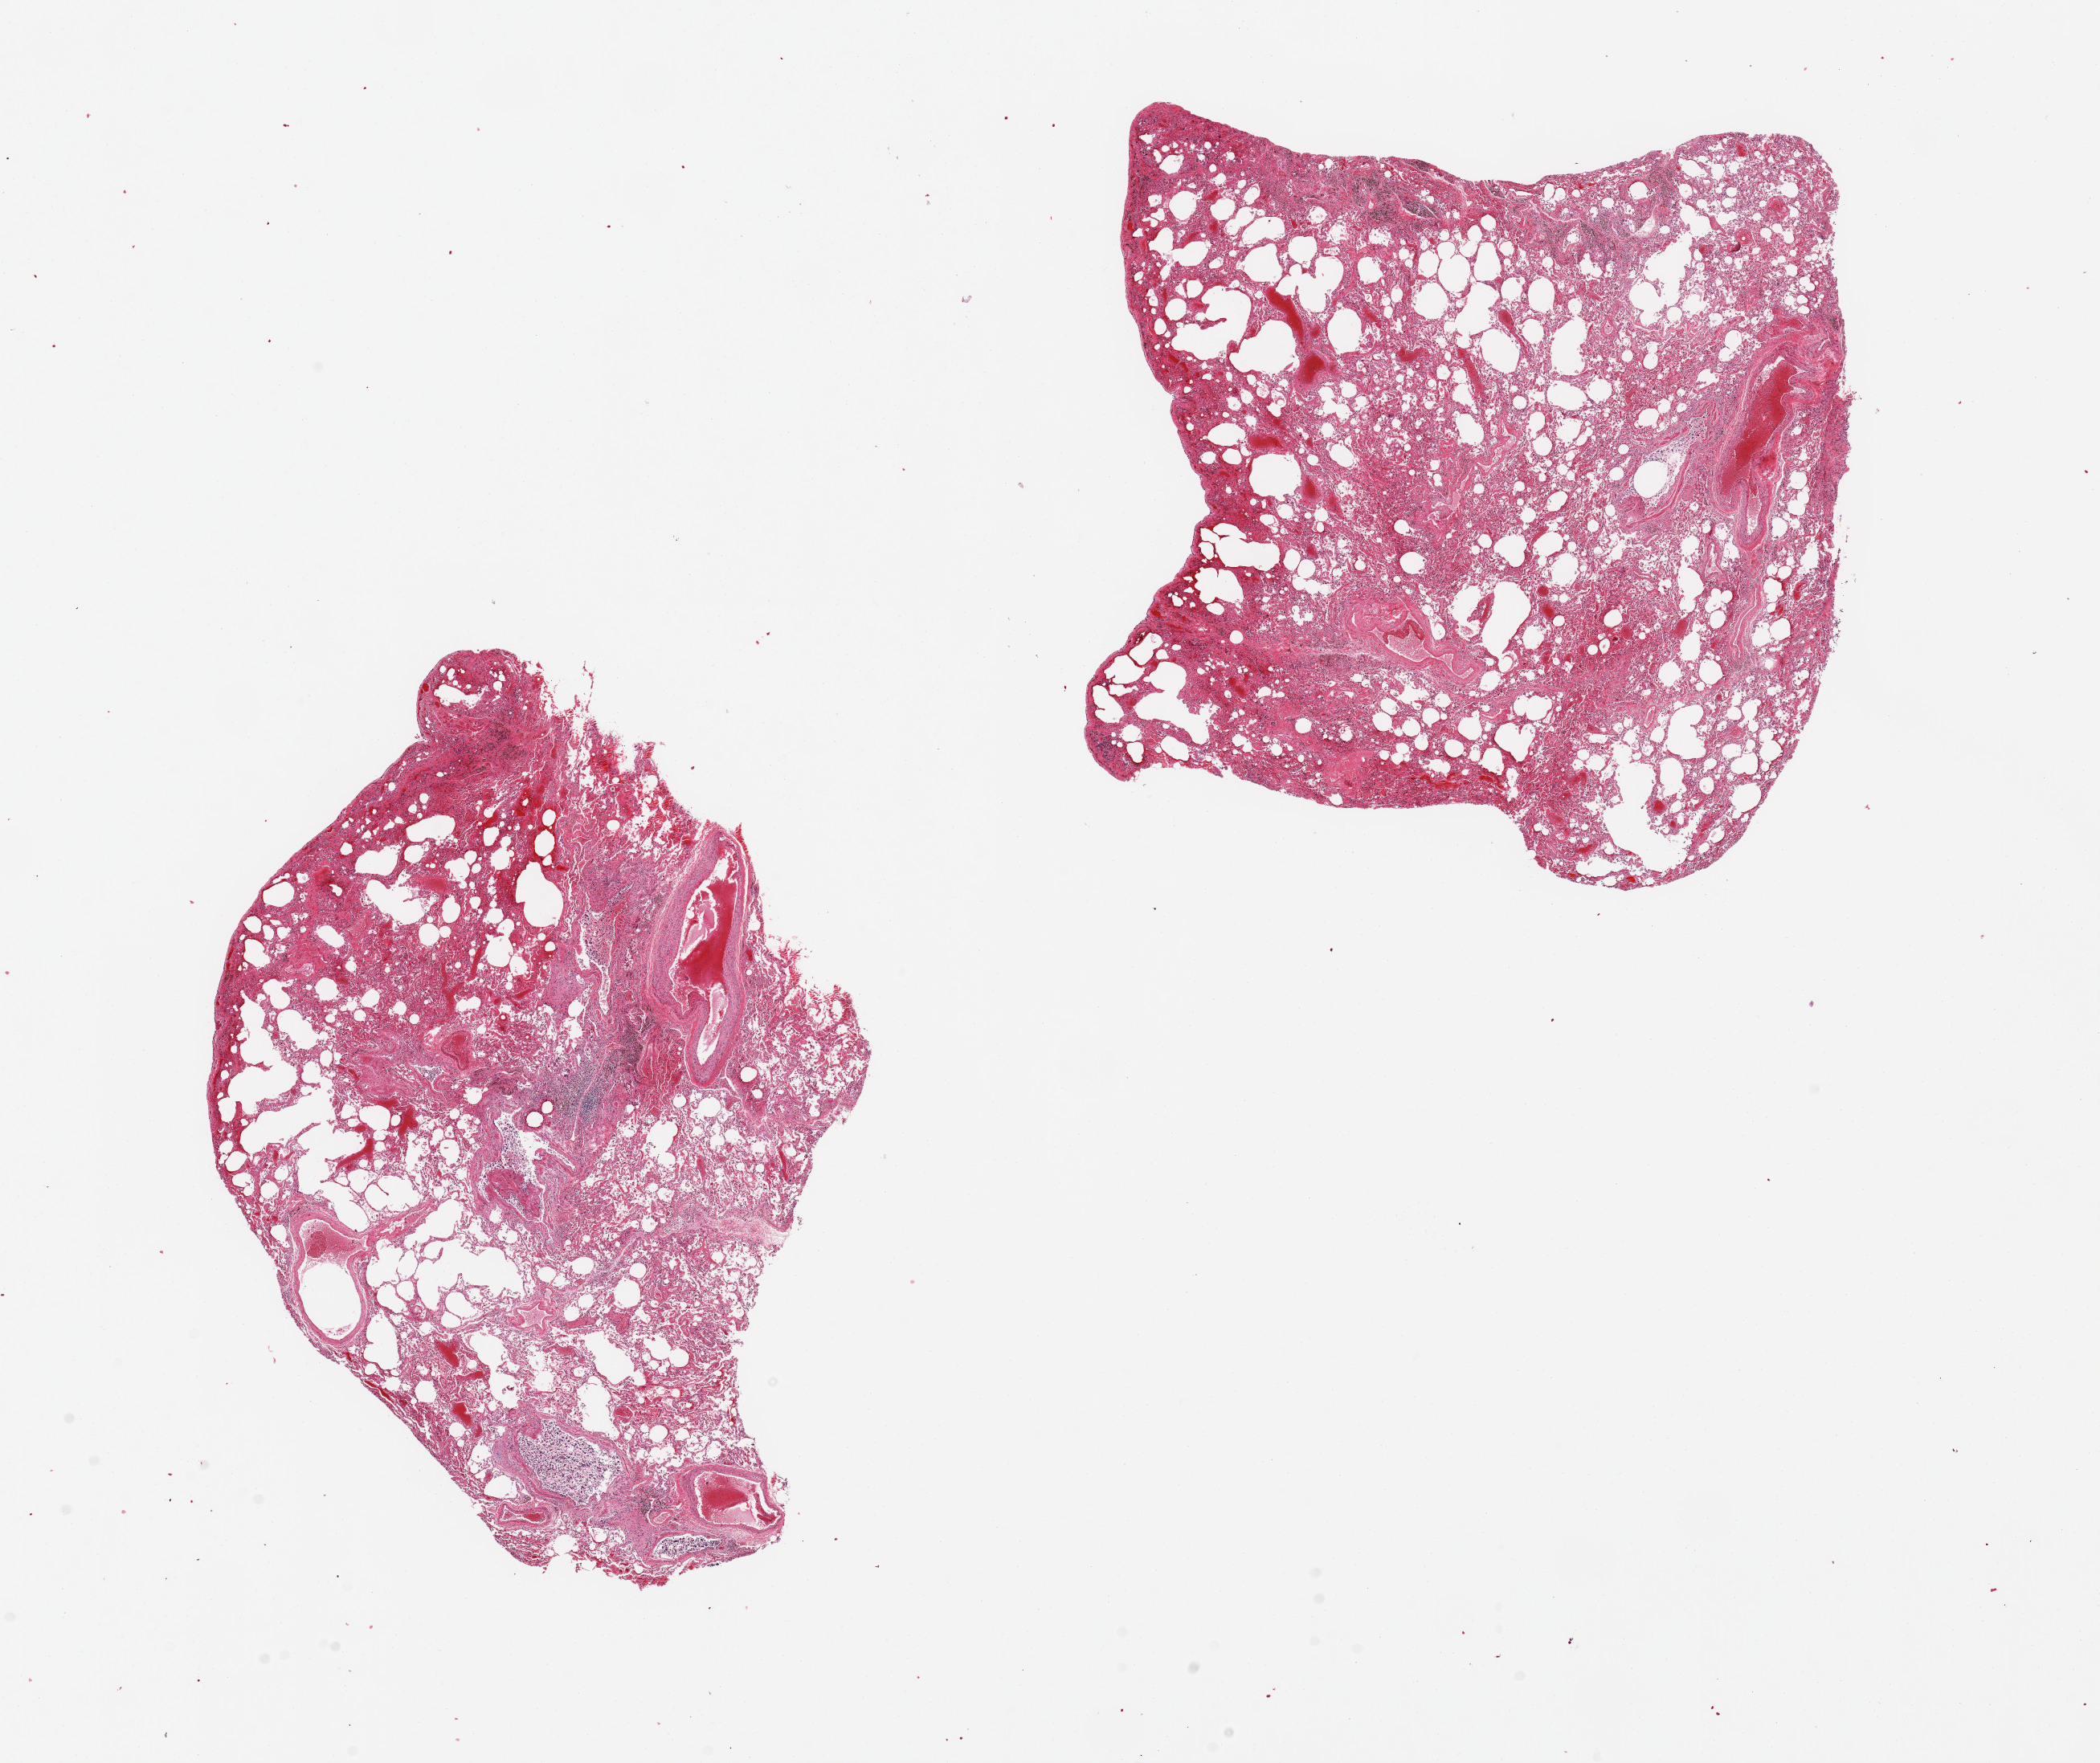
H&E whole-slide image, low-resolution overview of the scanned area, about 20.7 x 17.4 mm (from a 20x scan); PAXgene-fixed, paraffin-embedded tissue; sampled site (target tissue): lung; tissue donor sample. Donor: female.
Reviewer comment on this tissue sample: 2 pieces. 9x6.5 & 8x7mm; emphysema, patchy fibrosis, congestion.